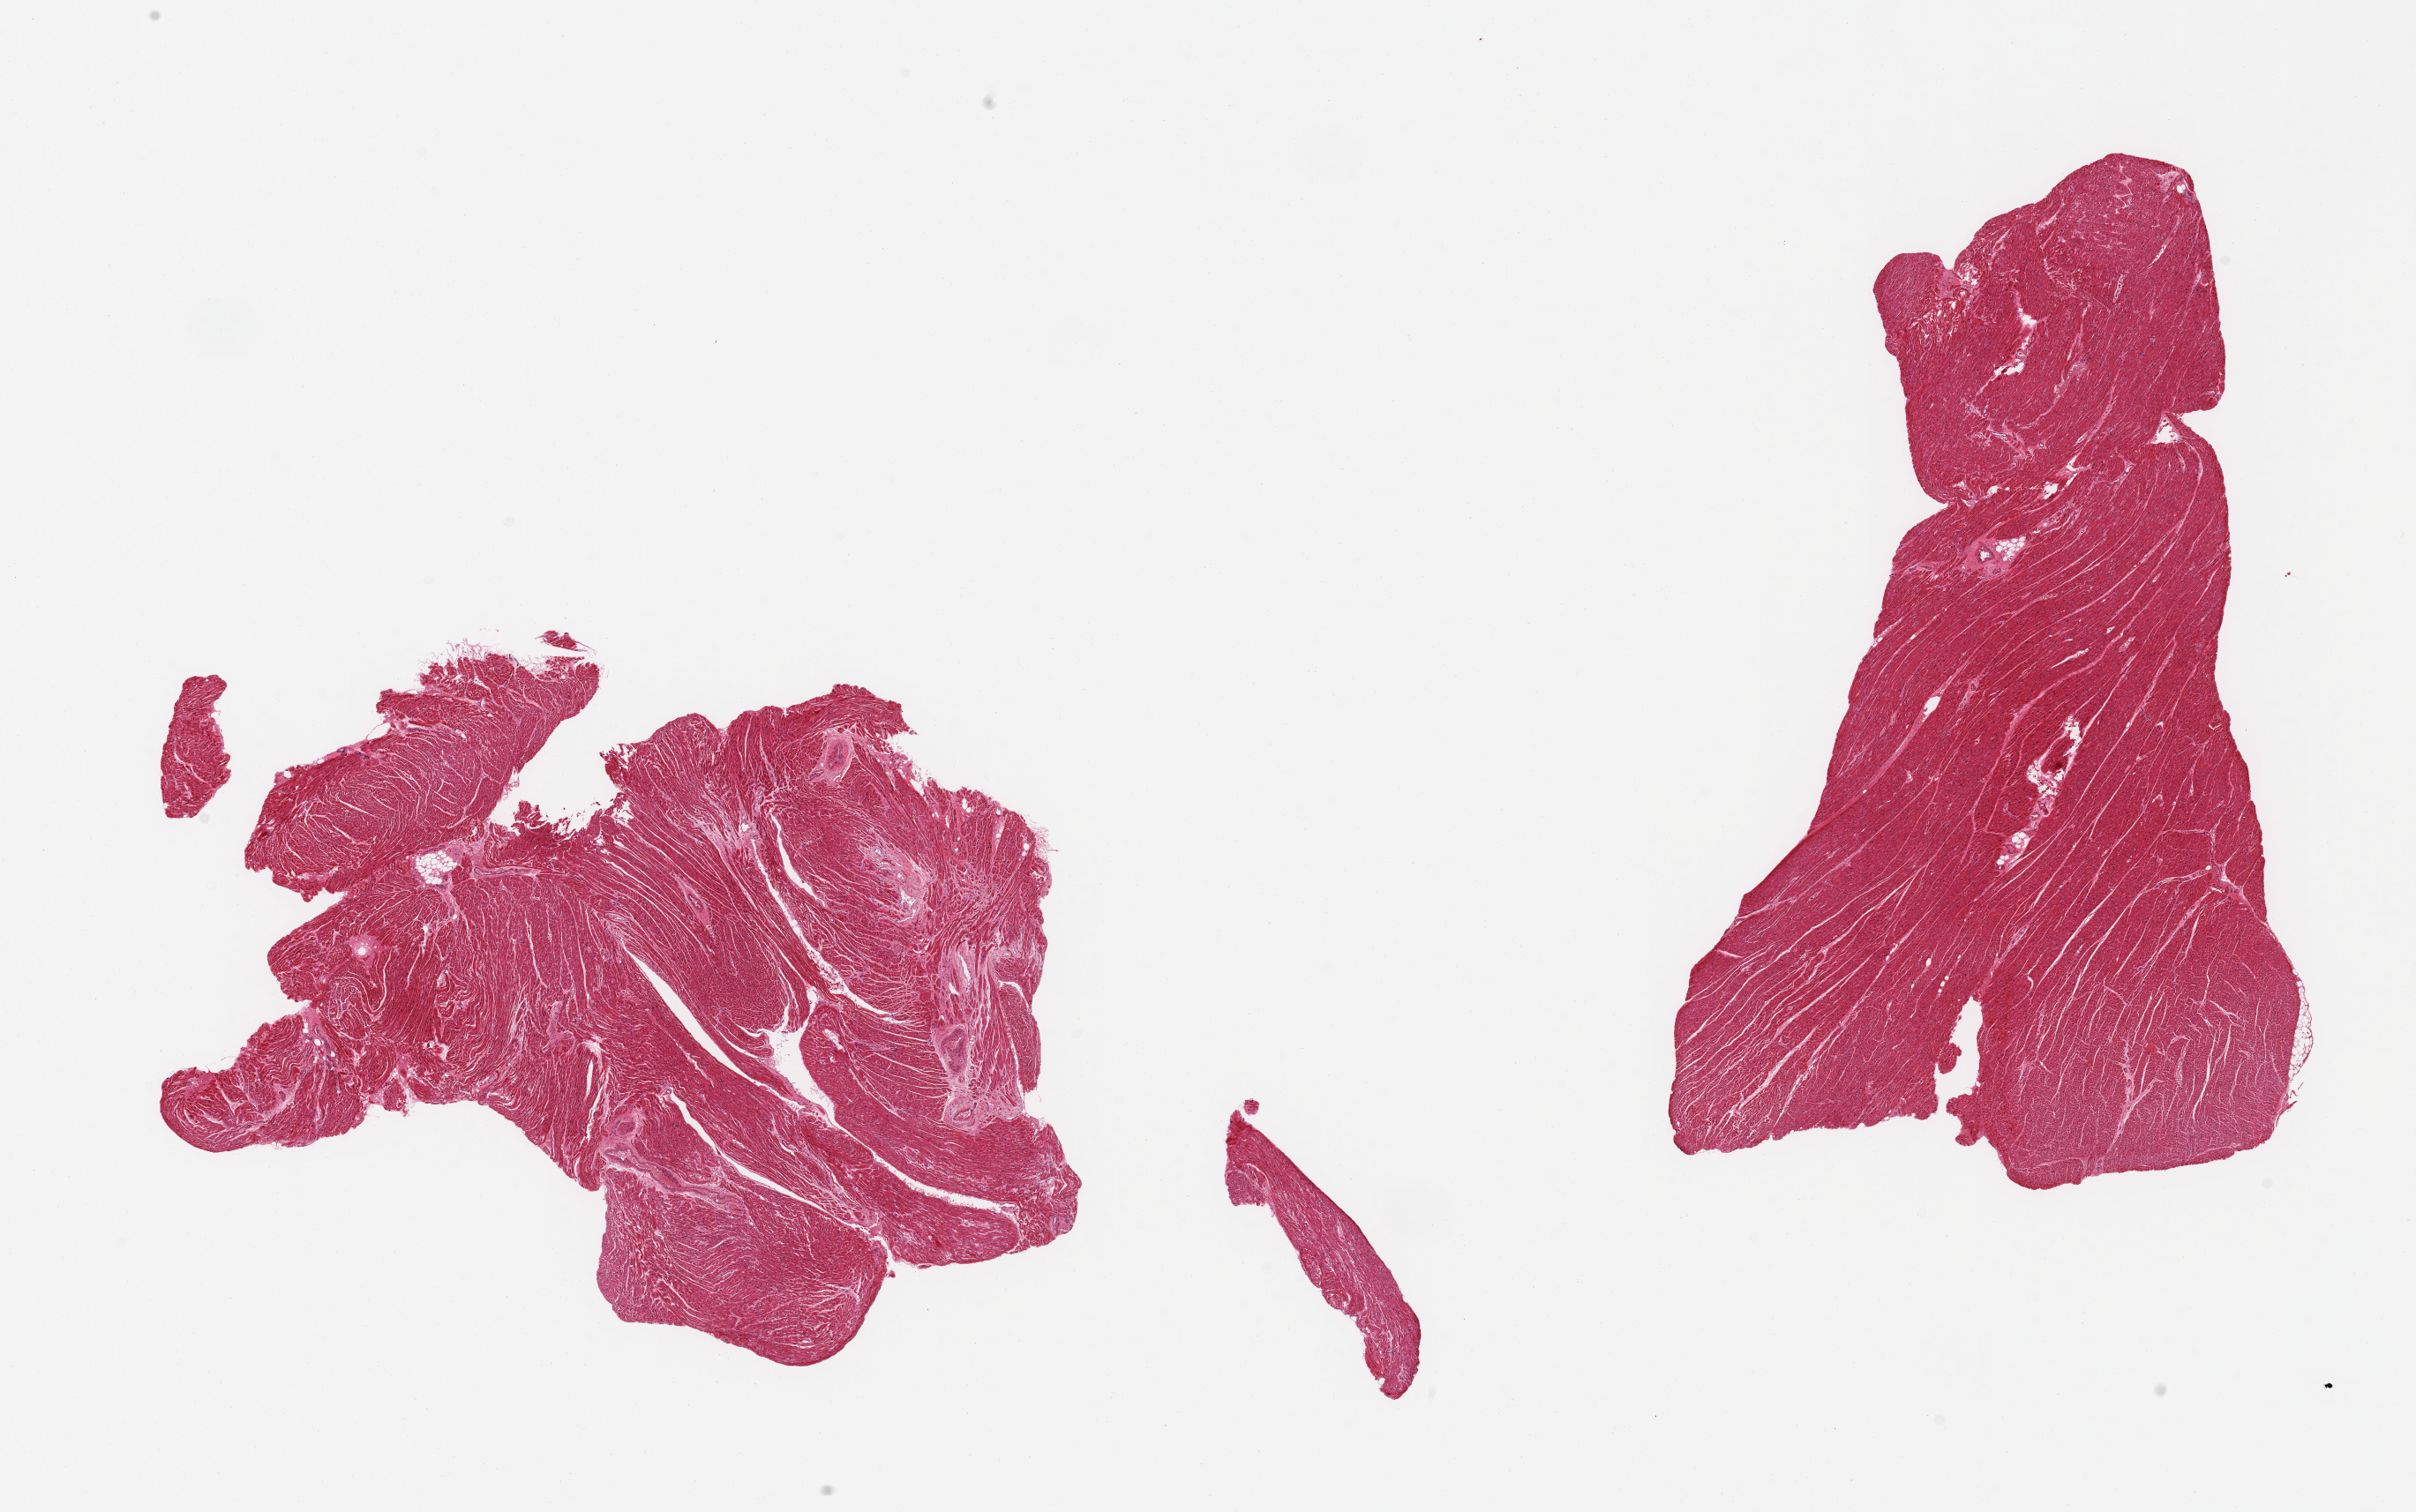
Digitized H&E-stained section — low-resolution overview of the scanned area, about 21.7 x 13.6 mm (slide scanned at 20x), PAXgene-fixed, paraffin-embedded tissue, section of heart (target tissue), tissue donor sample.
Reviewer comment on this tissue sample: 2 pieces.